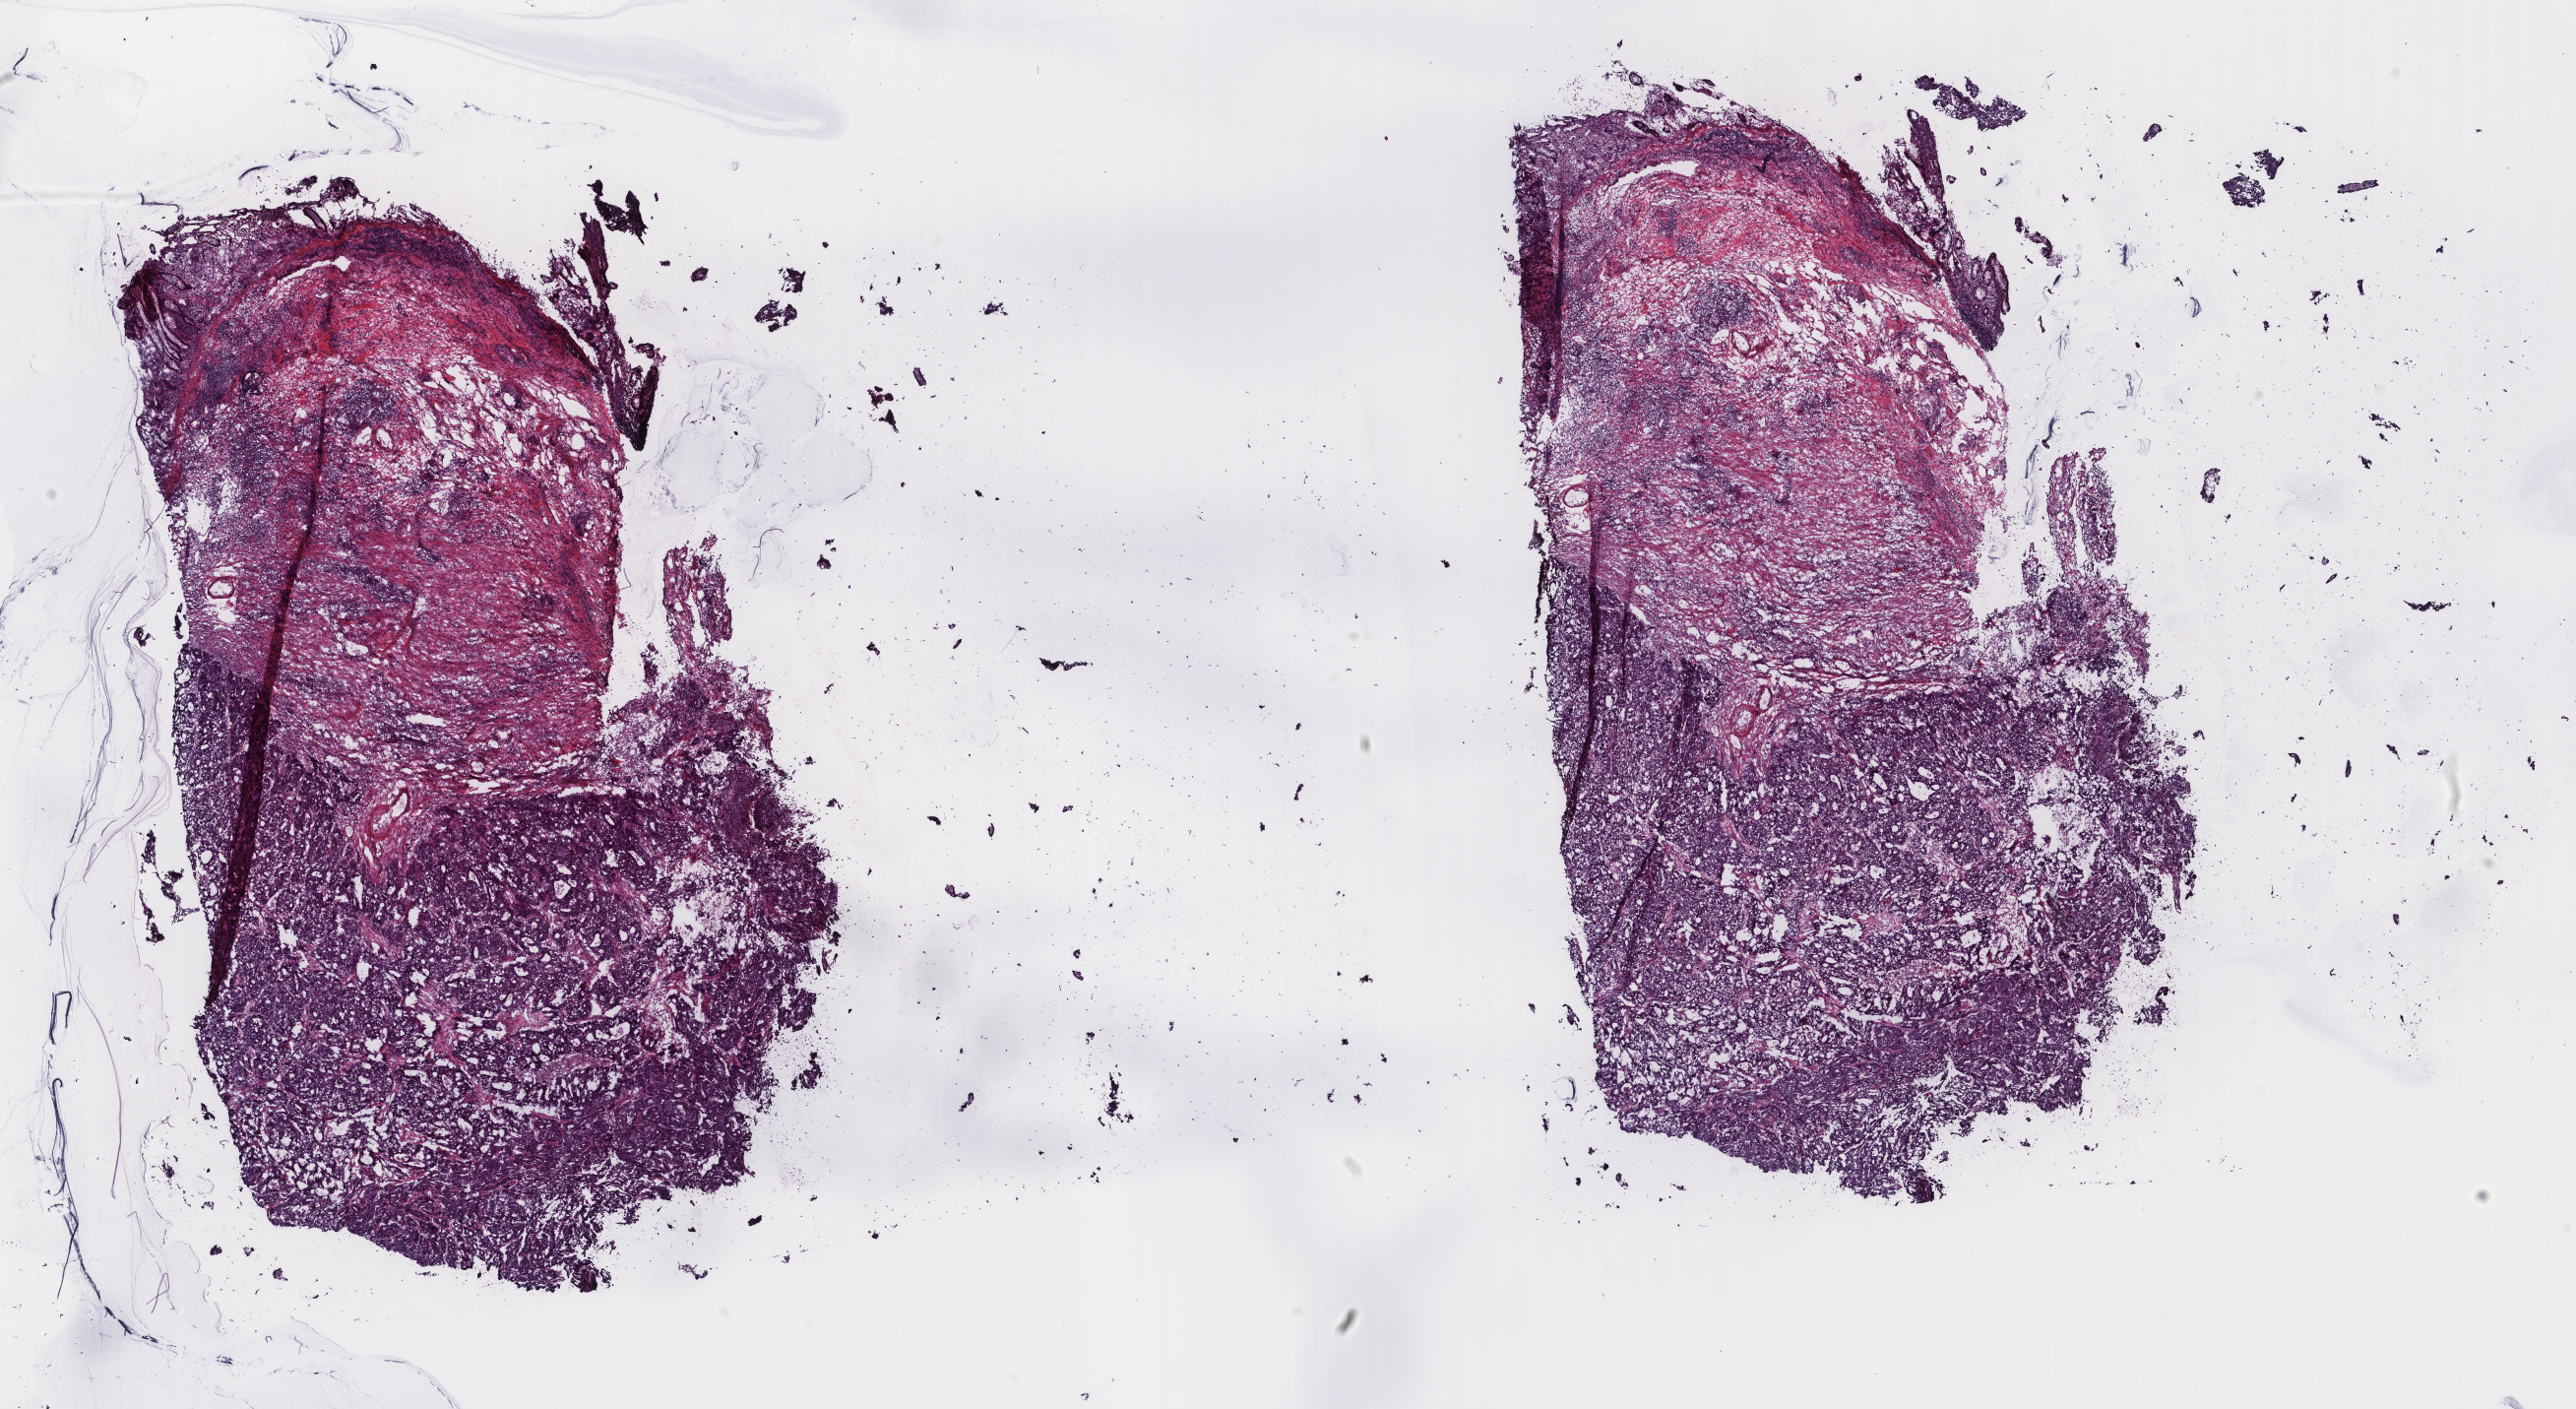
Whole-slide histology image, H&E — shown as a low-resolution overview of the whole scanned area (about 20.8 x 11.4 mm, slide scanned at 40x); frozen section; sample: primary tumour, colon. Patient: female, age at initial diagnosis 71 years. Pathologist review of this section (percent, as recorded): tumour cells 50%, tumour nuclei 75%, normal cells 10%, stromal cells 40%, necrosis 0%. Inflammatory infiltration, as recorded: lymphocyte infiltration 0%, monocyte infiltration 0%, neutrophil infiltration 0%.
• AJCC pathologic stage: IIIC
• histologic diagnosis: Adenocarcinoma, NOS (cecum)
• lymph nodes positive (case pathology): 5 of 13 examined